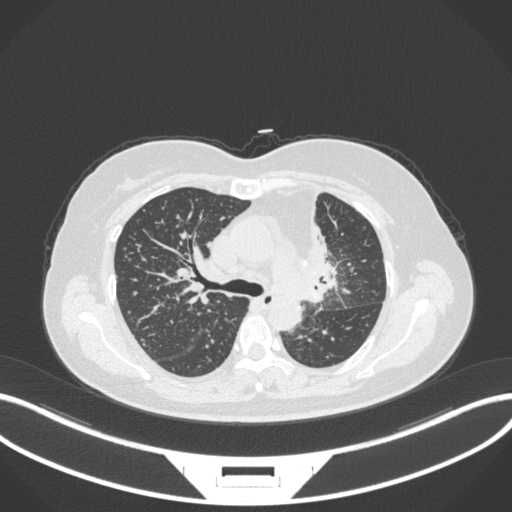
Chest CT, one axial slice. Position 219 of 348 along the scan axis. Reconstruction kernel B31f. 120 kVp. Lung window (W 1500 / L -600 HU). 512 × 512 image matrix, field of view 400 × 400 mm. Patient: female, 49 years. Case-level facts recorded for this patient, not image findings: clinical TNM (as recorded): T1c N0 M1.
Annotated regions visible in this slice (rectangle marked by the reading radiologist):
- lung tumour (recorded histology: adenocarcinoma): bounding box <295,191,344,302> (left, top, right, bottom; pixels)